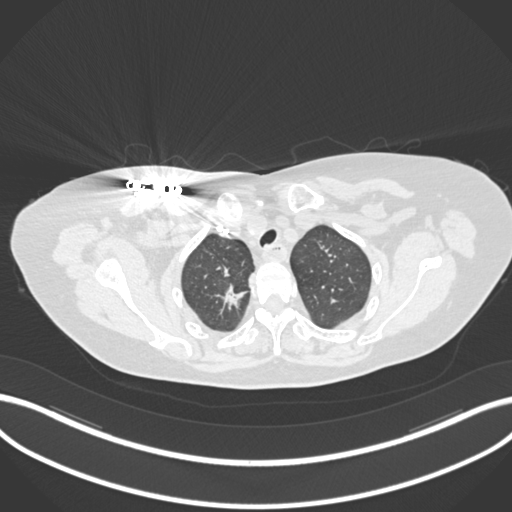
Chest CT, one axial slice. Reconstruction kernel B30f. 120 kVp. Lung window (W 1500 / L -600 HU). 1 mm slice thickness. 512 × 512 image matrix, field of view 400 × 400 mm. Patient: female, 72 years. From the clinical record (not read from this slice): clinical TNM (as recorded): T1c N0 M0.
Outlined on this slice (bounding box drawn by a radiologist):
- lung tumour (recorded histology: adenocarcinoma): bounding box <215,280,251,314> (left, top, right, bottom; pixels)